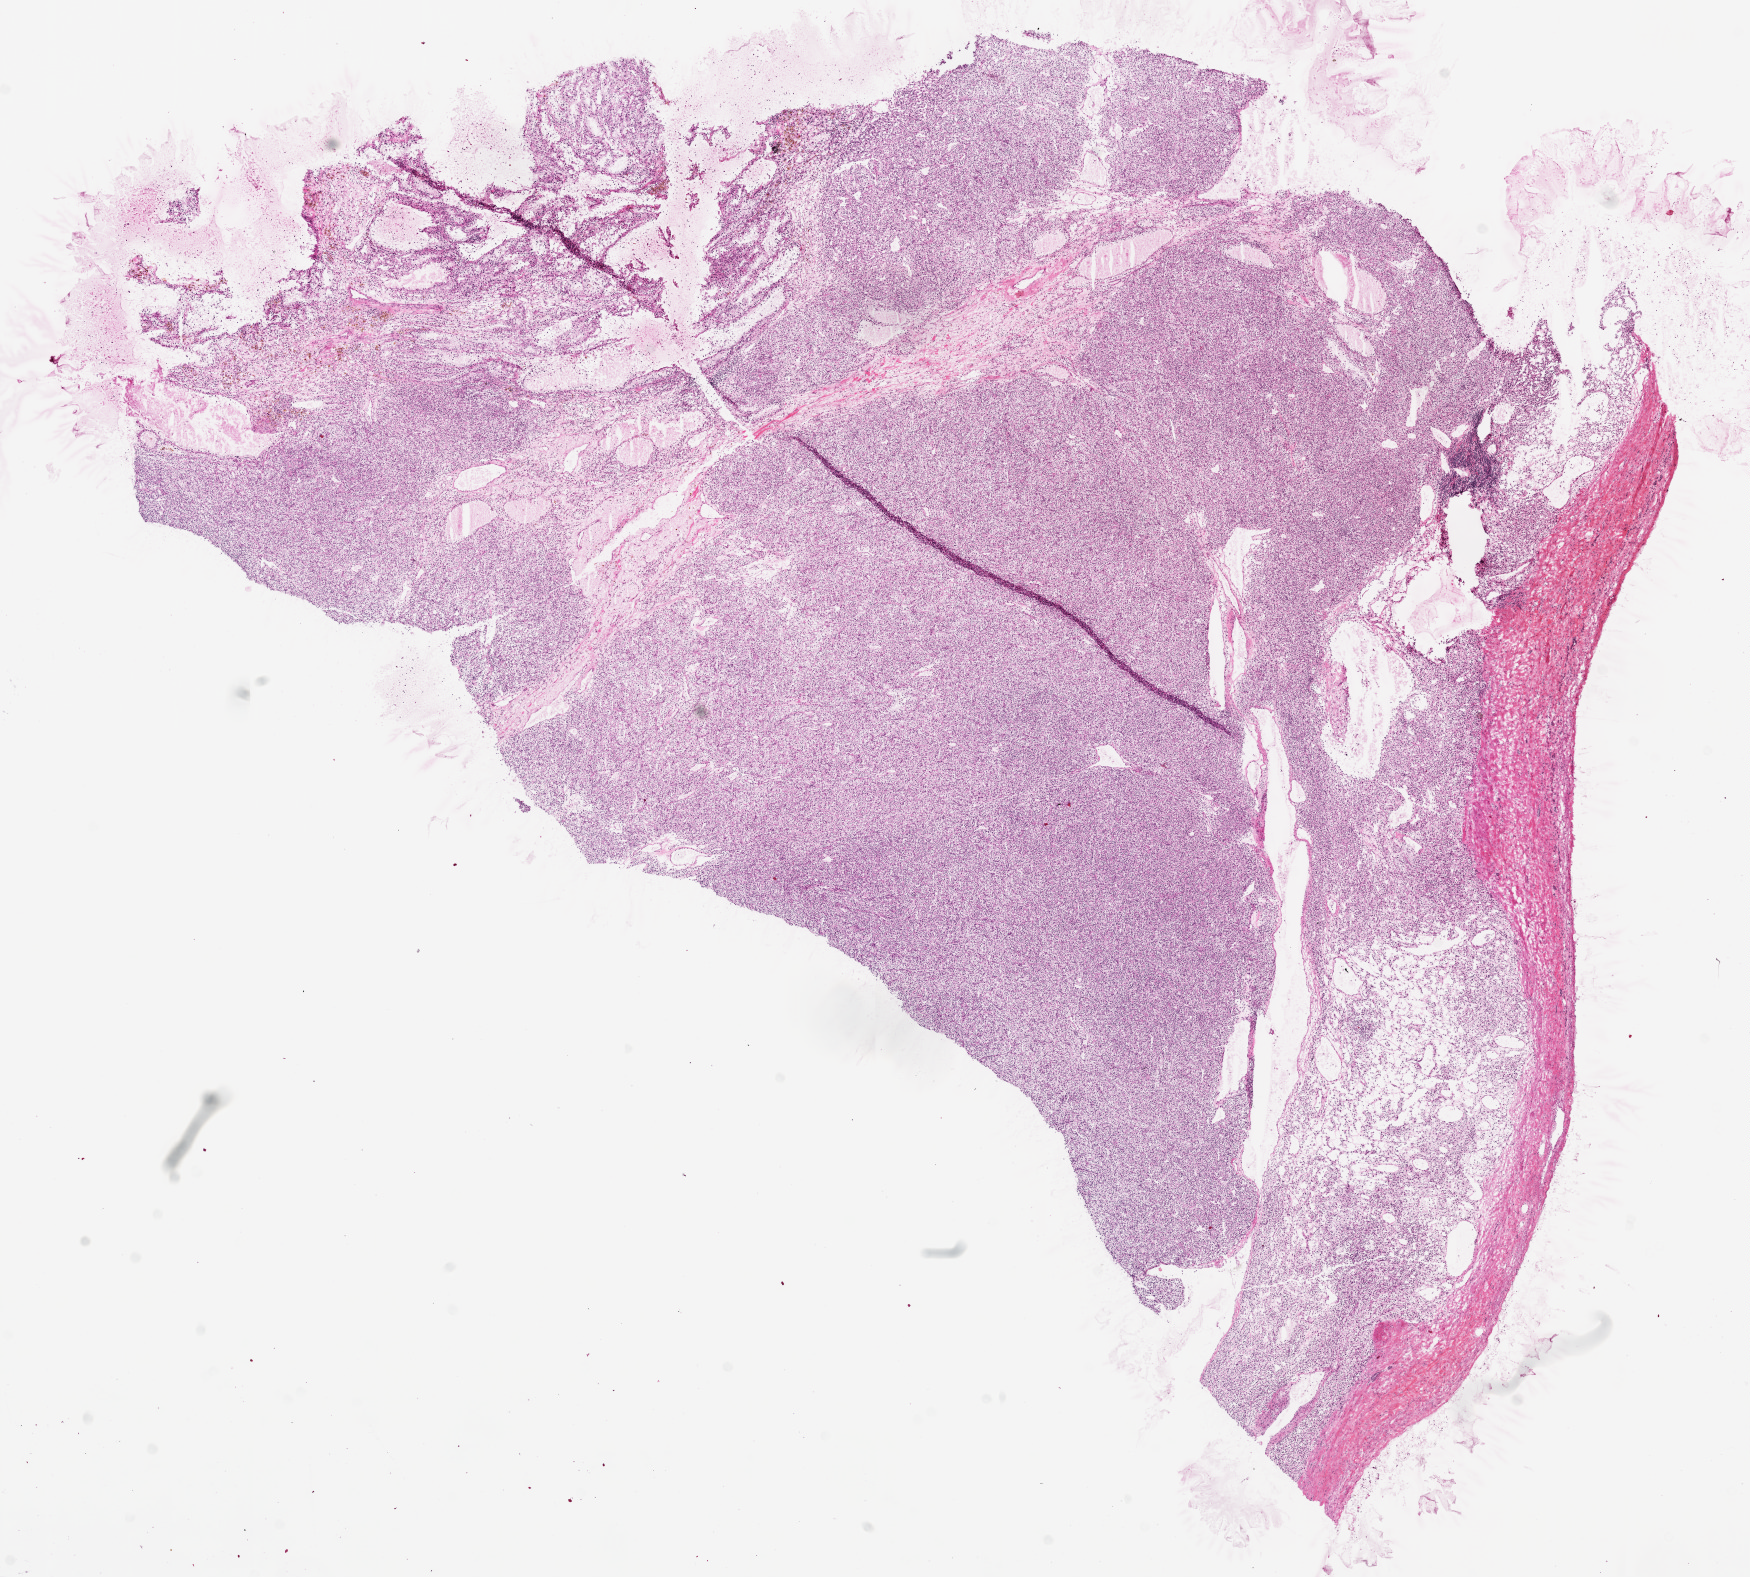
Whole-slide histology image, H&E-stained, shown as a low-resolution overview of the whole scanned area (about 14.0 x 12.7 mm, slide scanned at 20x); frozen section from the top of the tissue portion; primary tumour sample from the kidney. Patient: female, age at initial diagnosis 68 years. Histologic grade: G3 (poorly differentiated). Slide review estimates, as recorded: tumour cells 90%, tumour nuclei 95%, normal cells 0%, stromal cells 10%, necrosis 0%. Infiltration values recorded for this section: lymphocyte infiltration 1%, monocyte infiltration 0%, neutrophil infiltration 0%.
Diagnosis: Clear cell adenocarcinoma, NOS. AJCC pathologic stage: IV (7th edition).